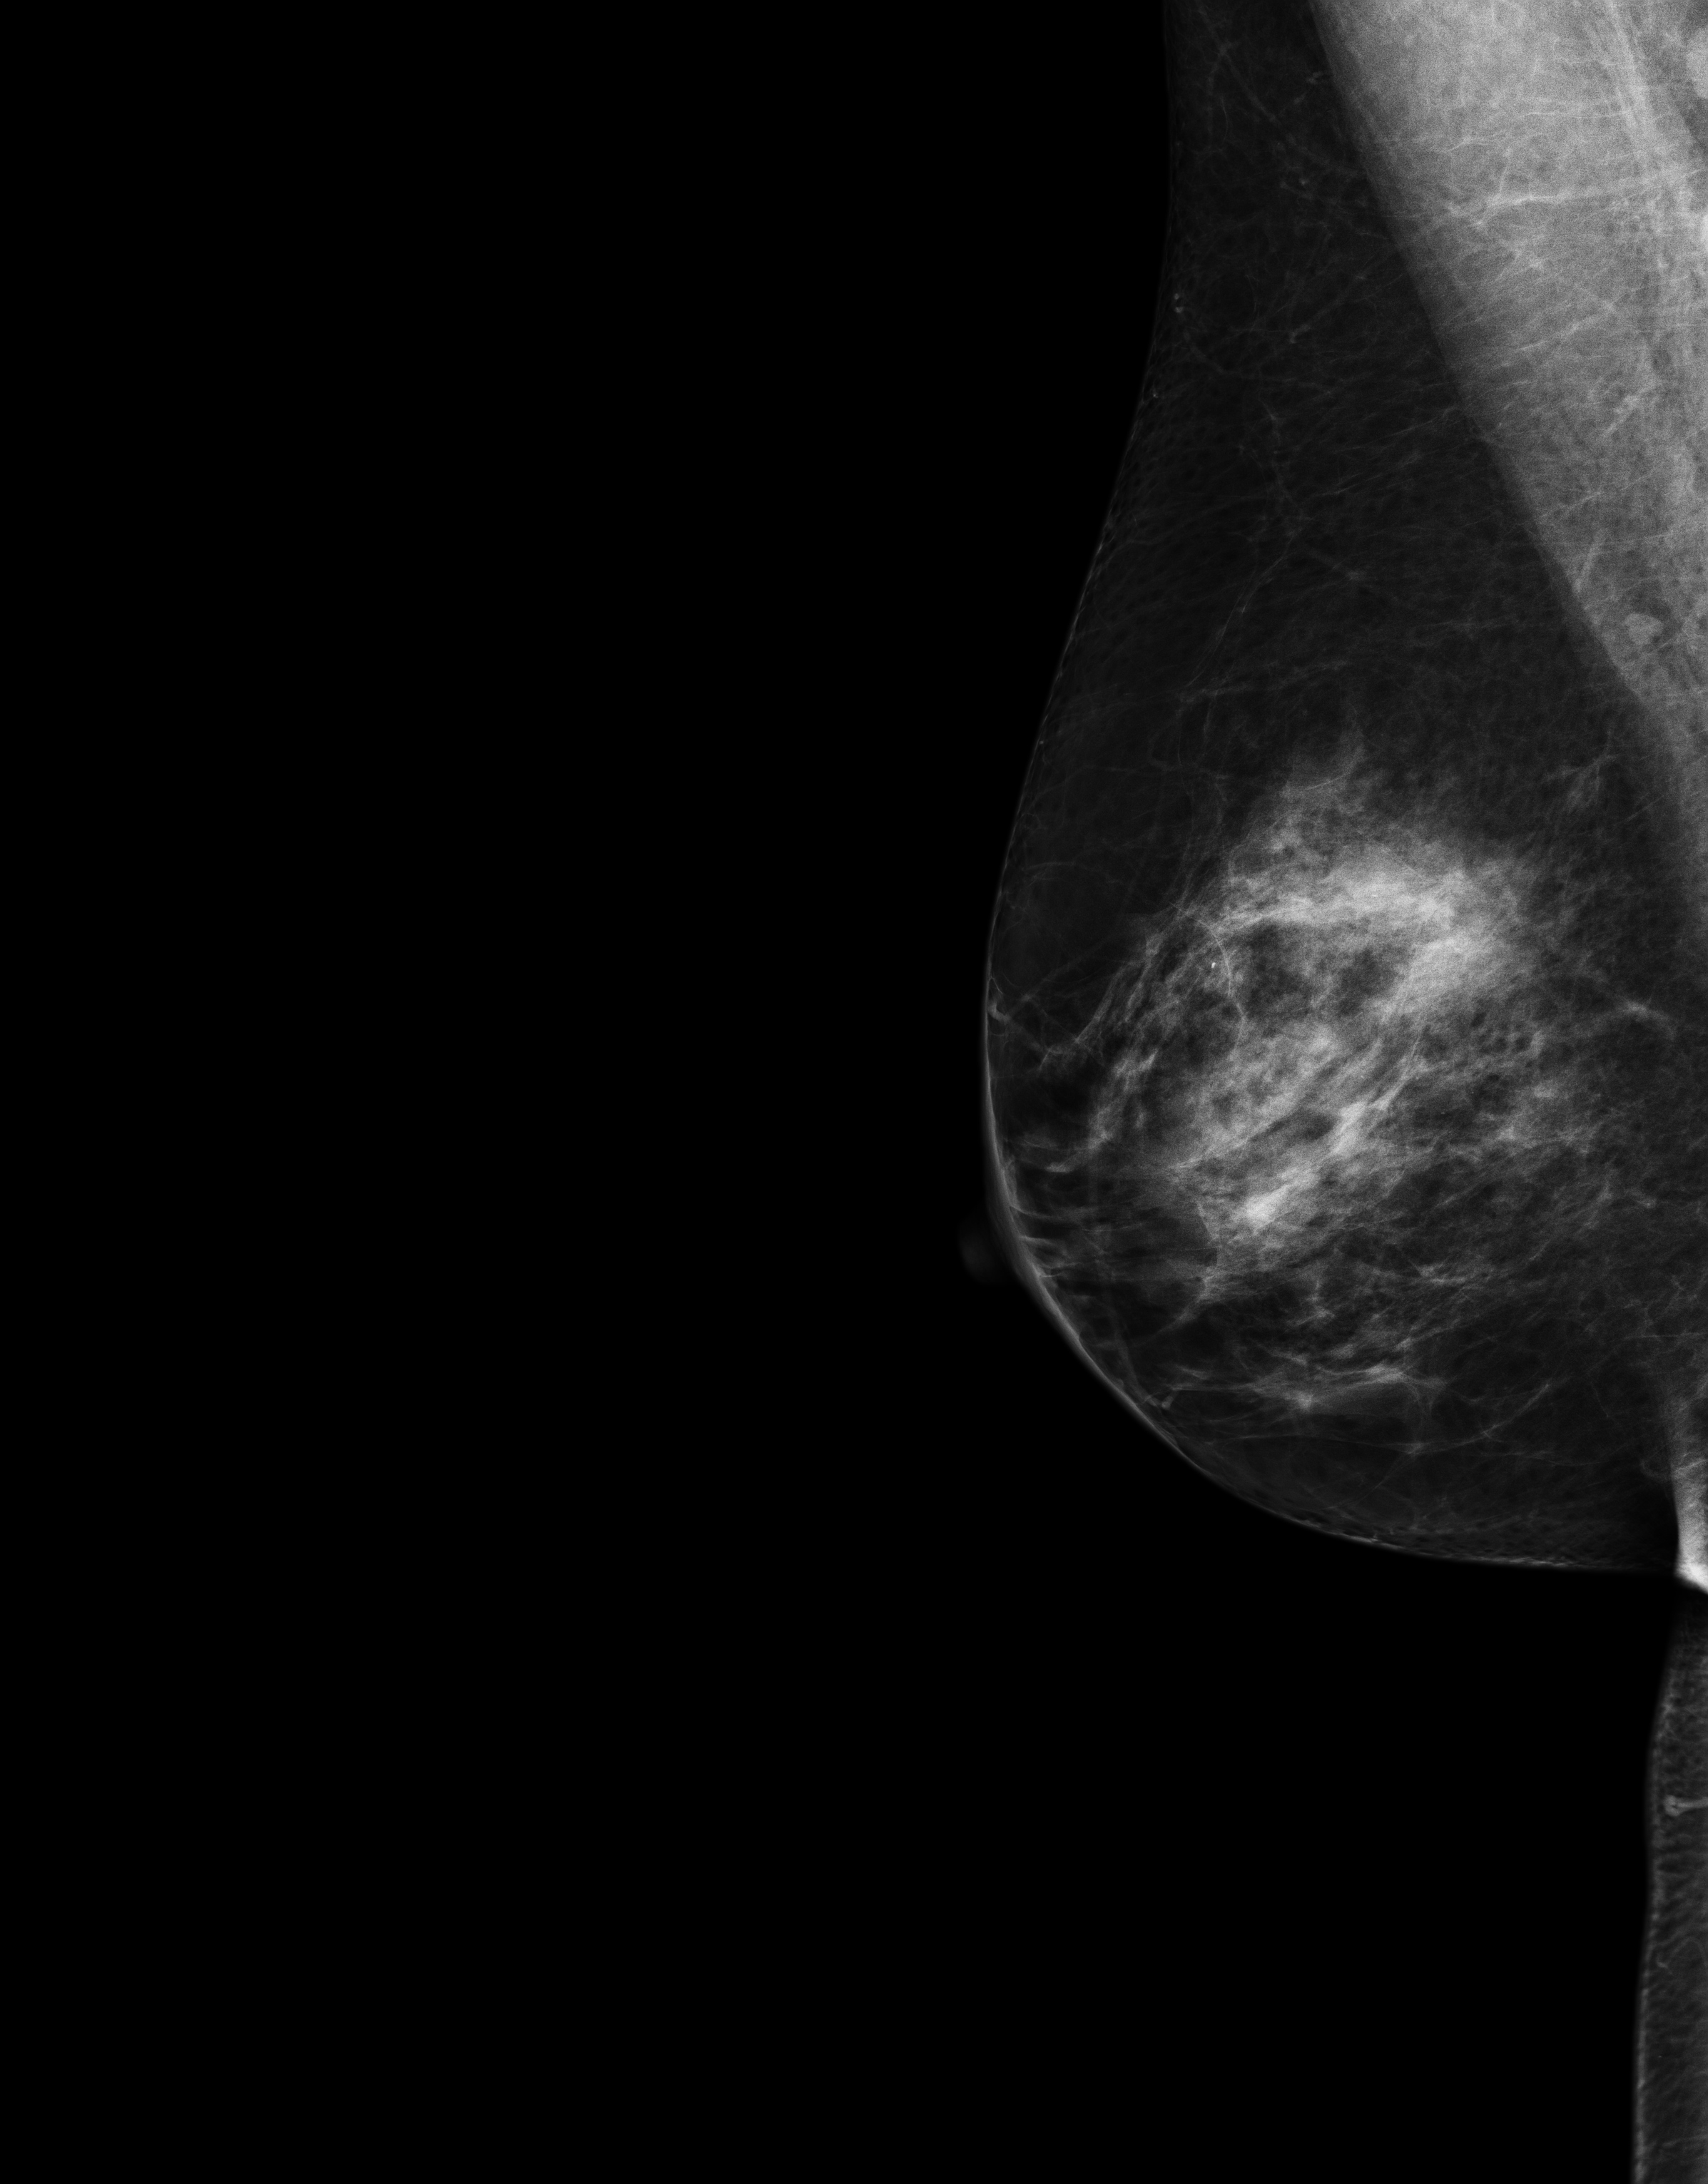
Annual screening mammography examination. Patient: female, 46 years.
Image type: full-field digital mammogram. Breast: right. Projection: MLO view.